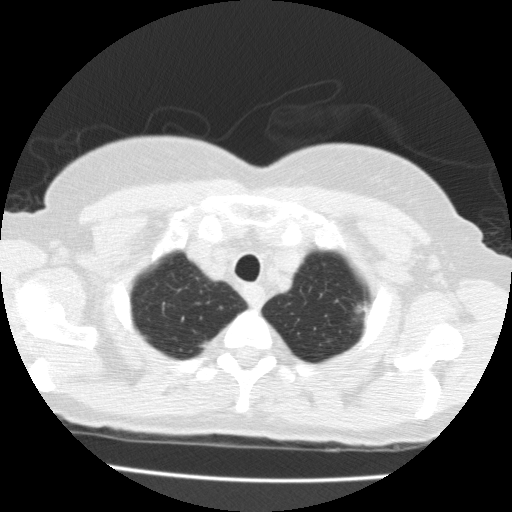
Low-dose screening chest CT, one axial slice; slice 163 of 183 in the series (ordered by position); reconstruction kernel FC10; 120 kVp; lung window (W 1500 / L -600 HU); 512 × 512 image matrix, field of view 320 × 320 mm.
Outlined on this slice (outlined manually by an expert reader):
- lesion 1 (tumor, upper lobe of left lung): box from (x=357, y=305) to (x=363, y=313) px